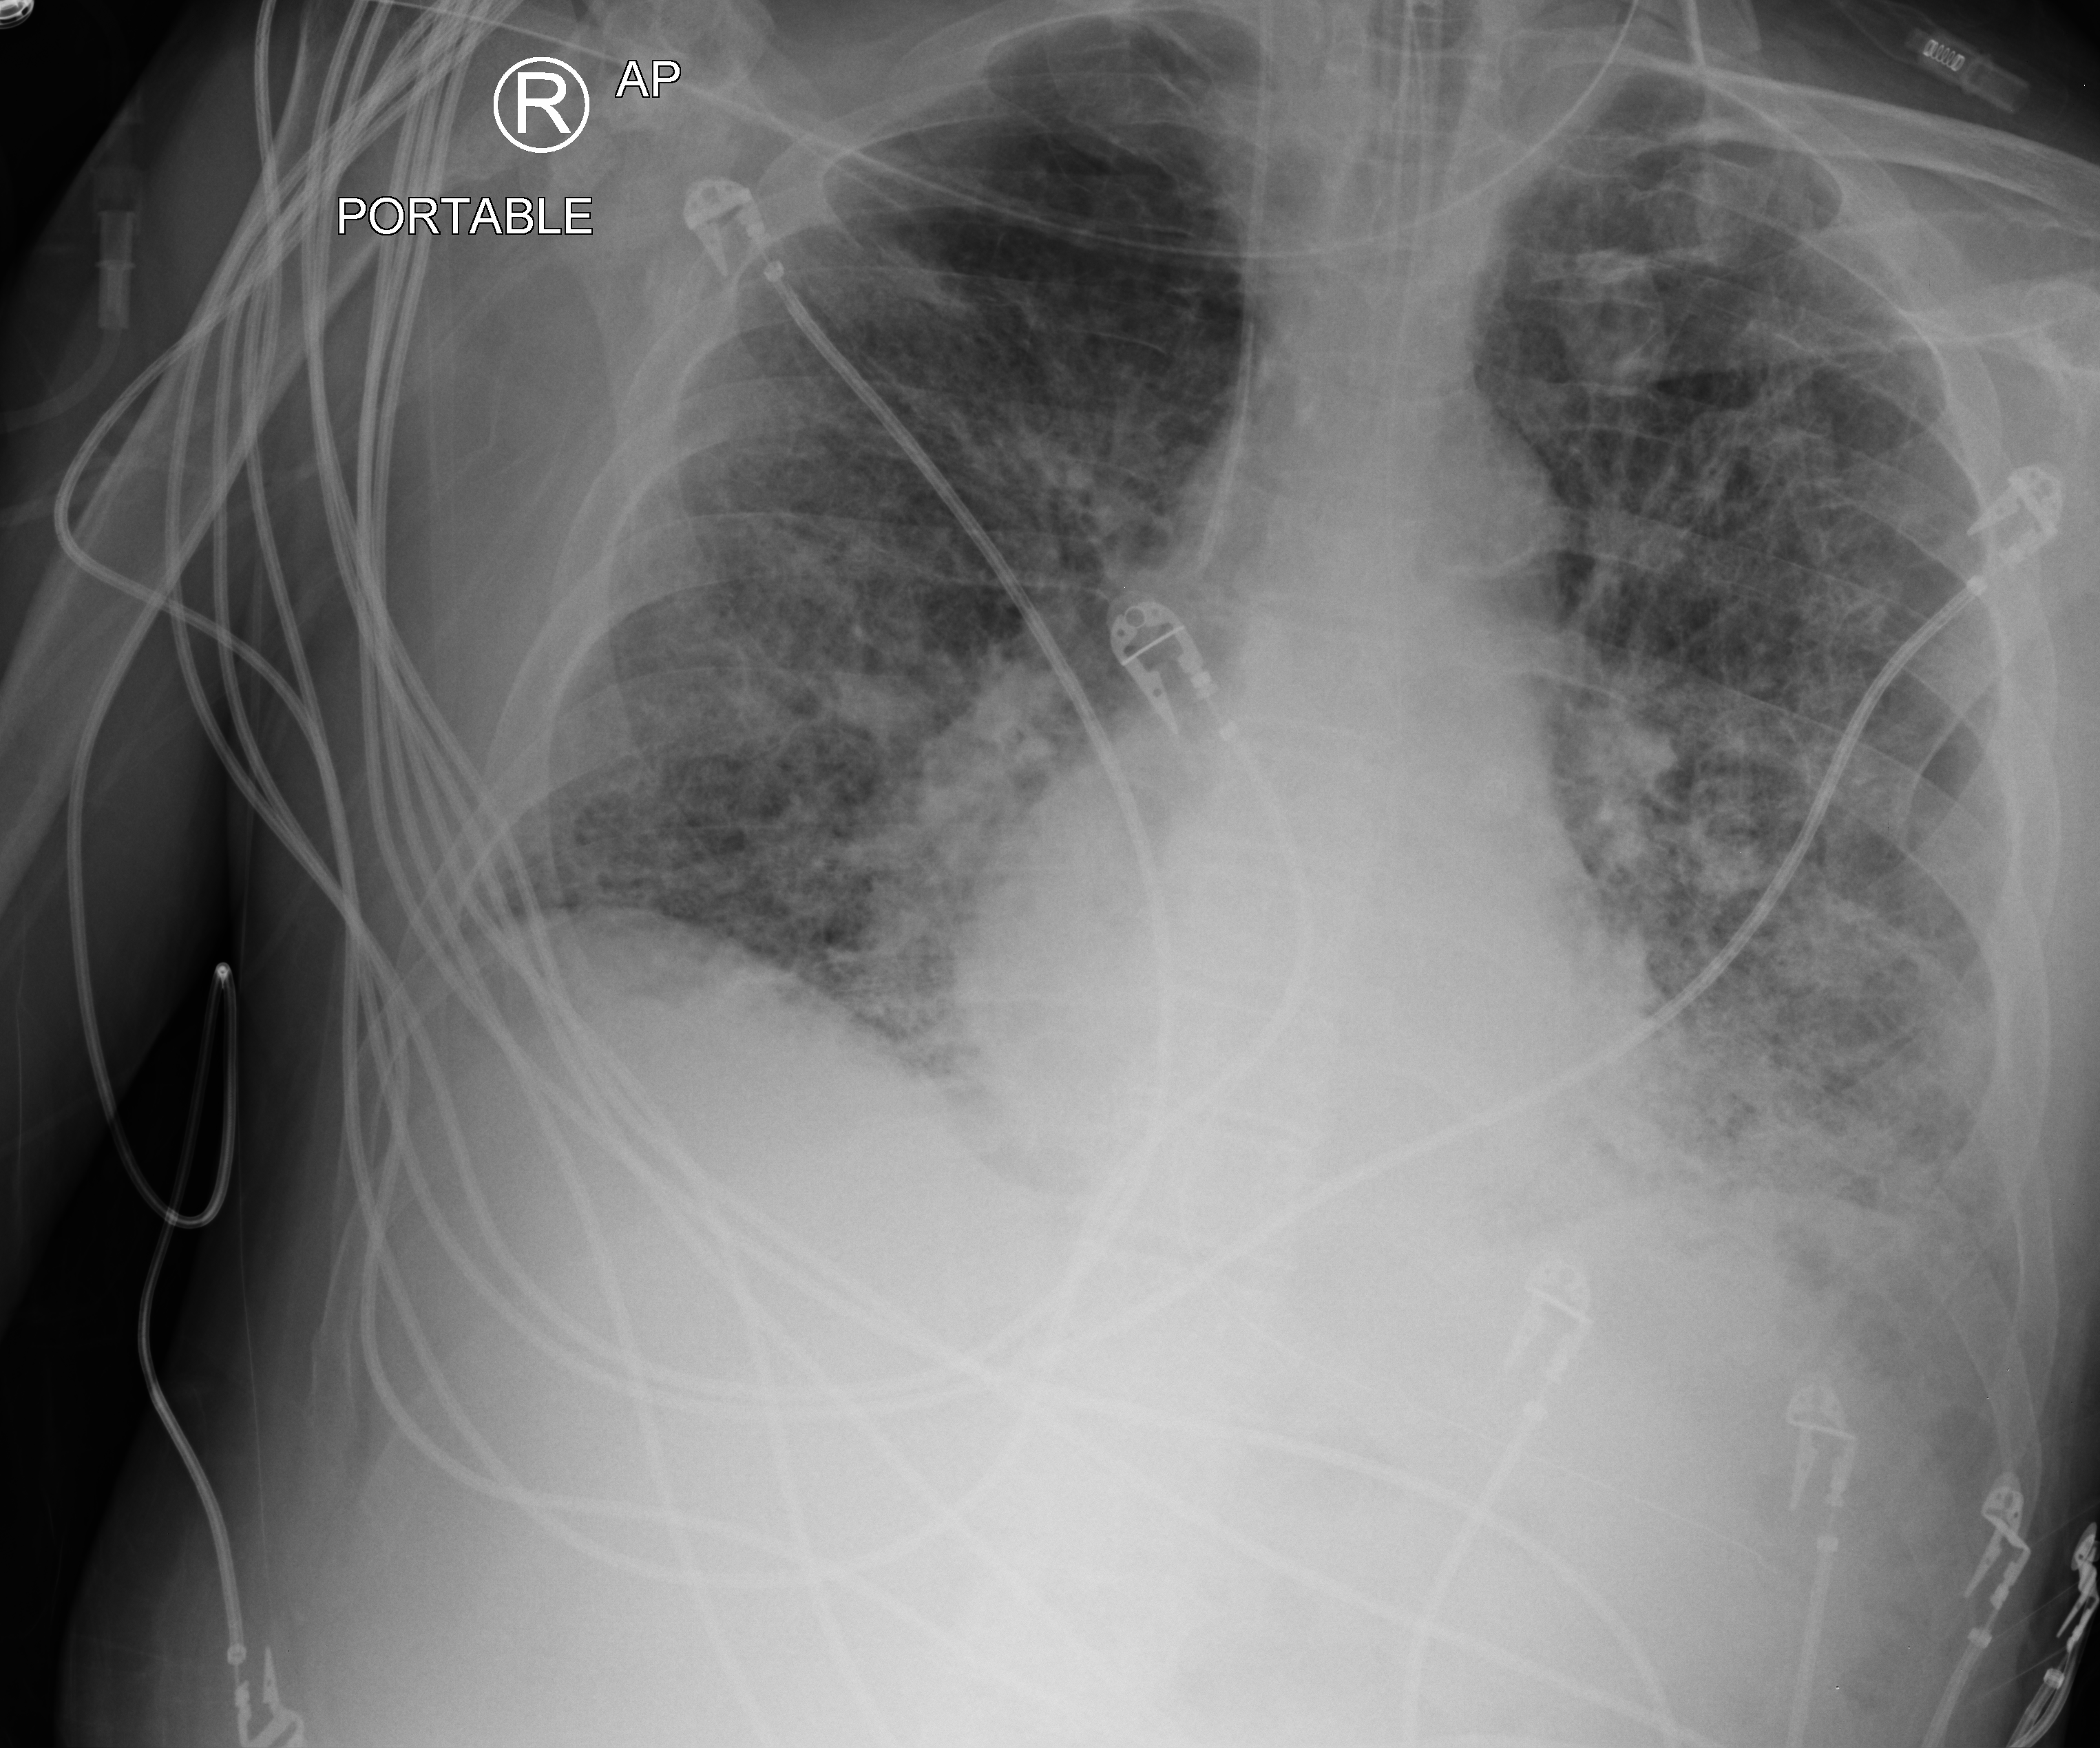
Portable chest radiograph; anteroposterior (AP) projection. Patient hospitalised with COVID-19; male, aged 75–90 years.
Hospital-stay facts (about this admission, not read from this image; timing relative to this image not recorded):
- admitted to intensive care during this hospital stay: yes
- length of hospital stay: 13 days
- mechanically ventilated during this hospital stay: yes